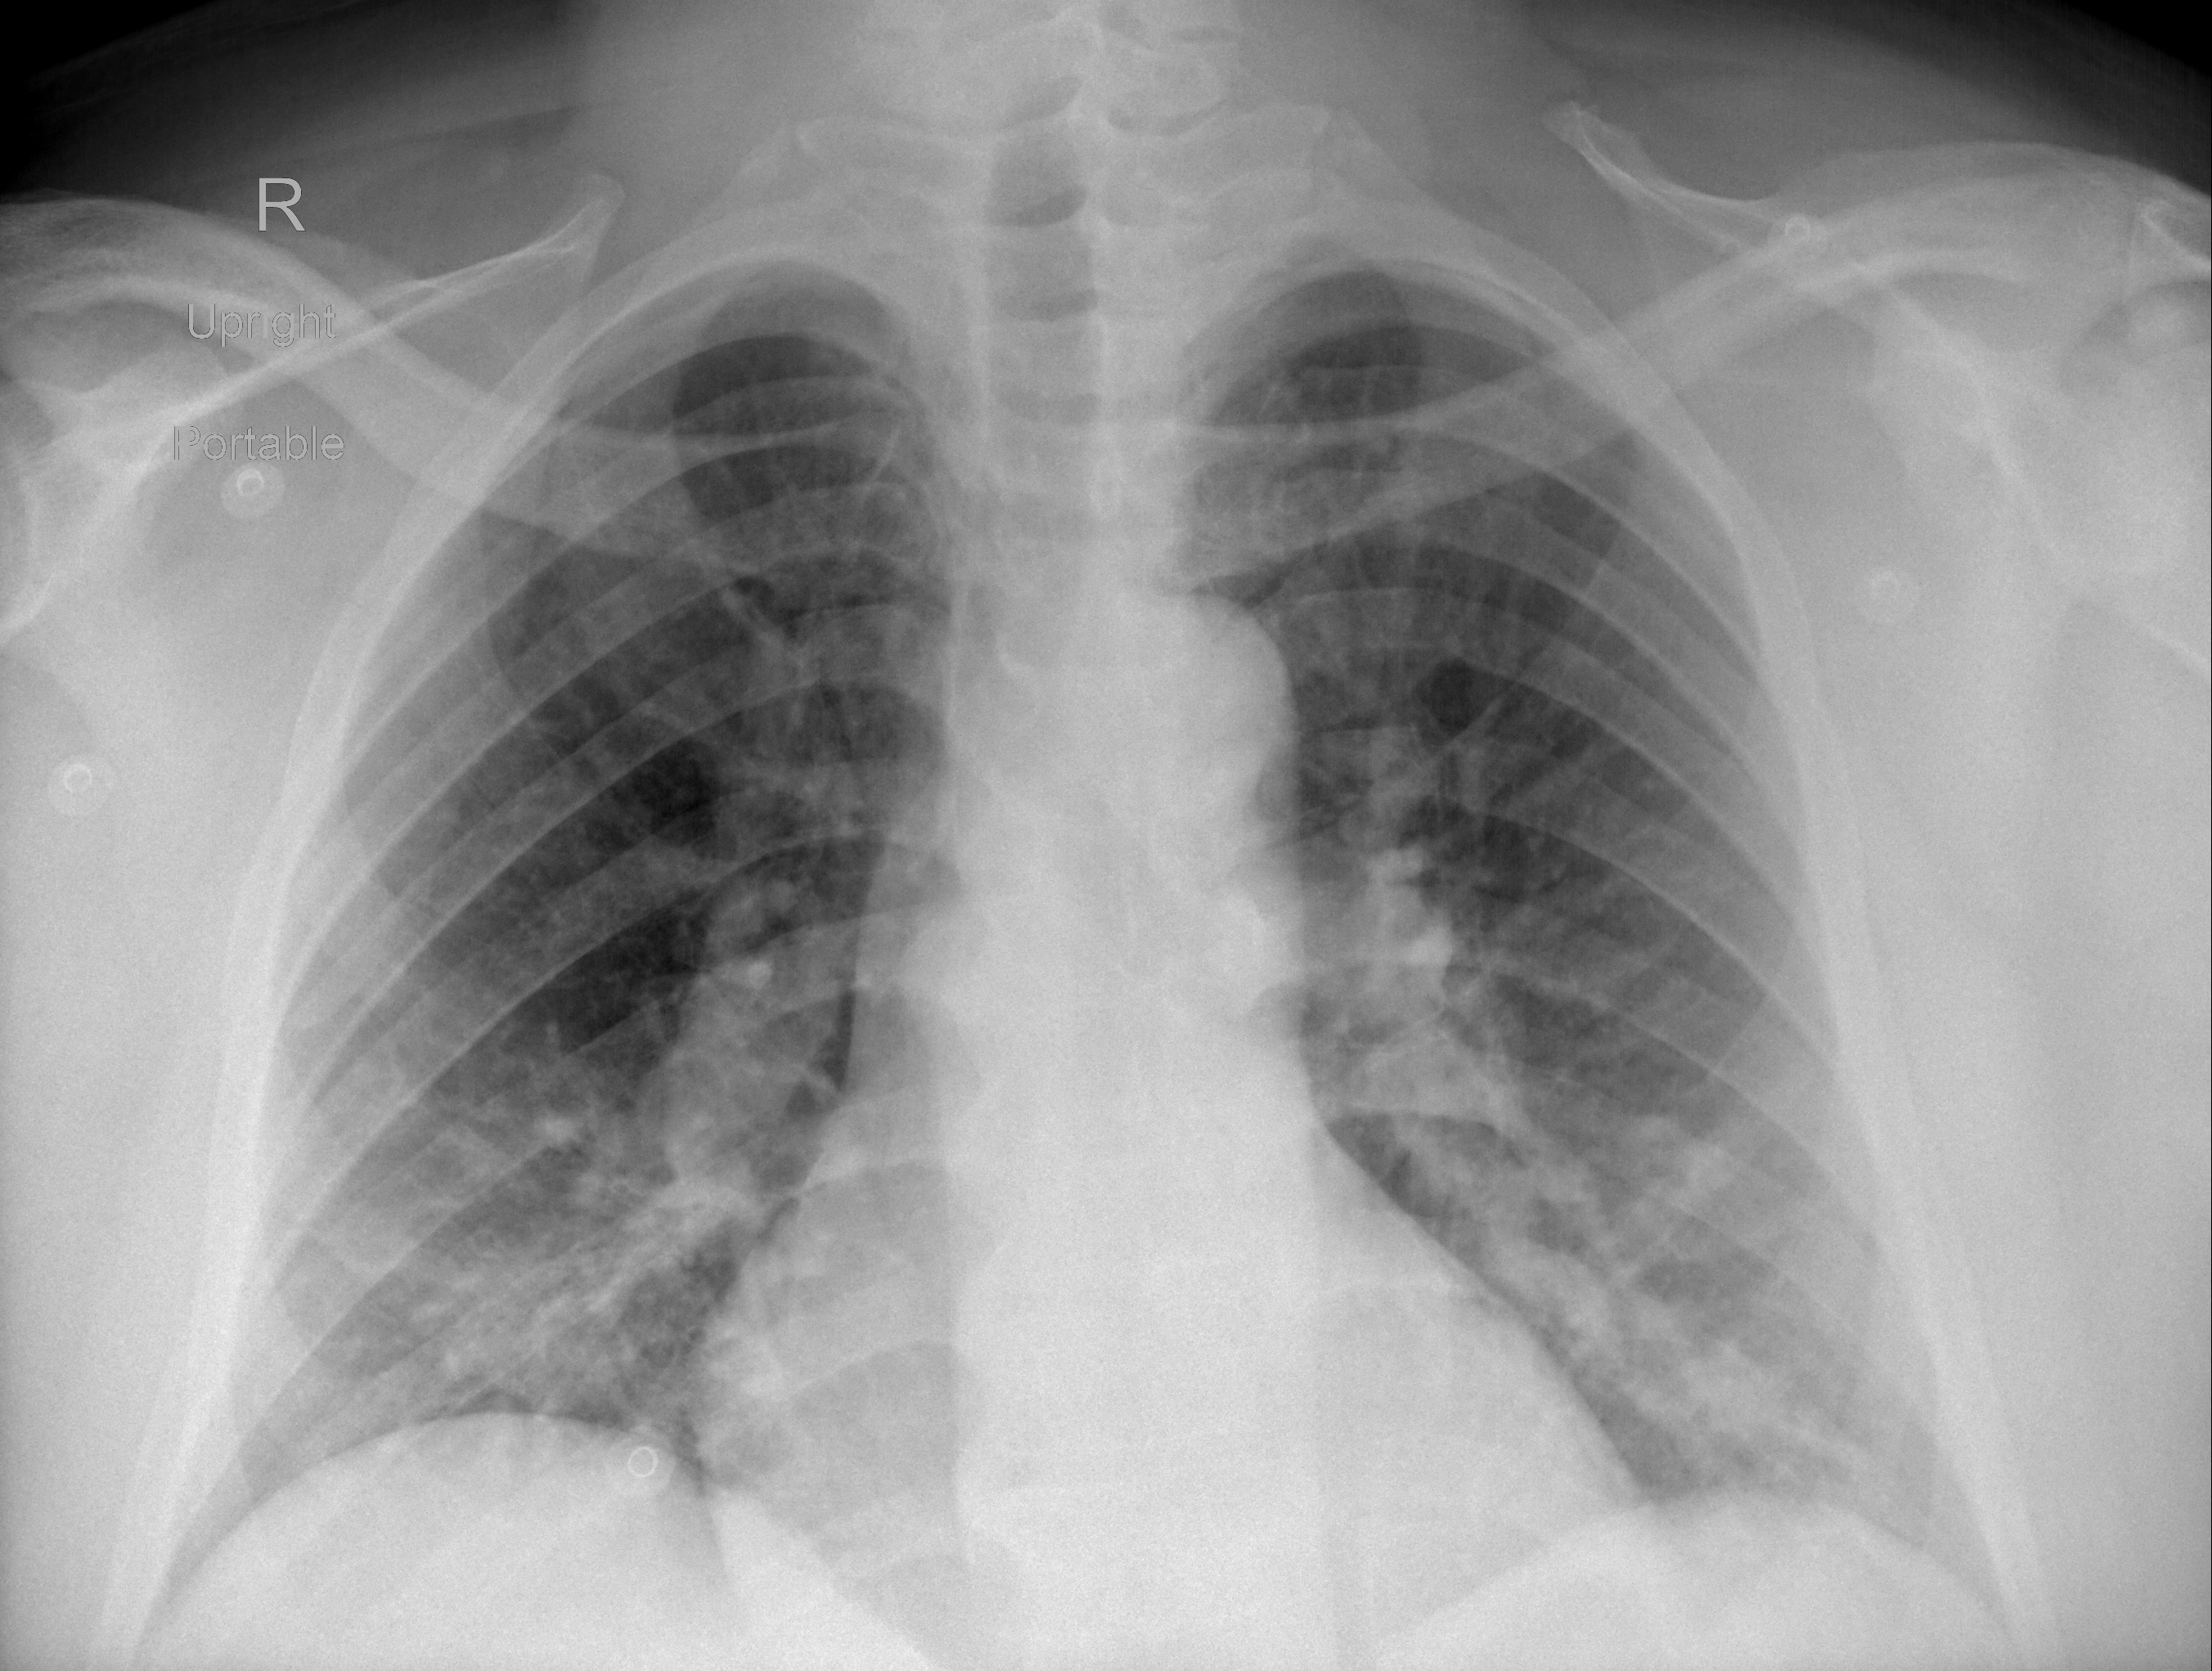
Chest X-ray (portable), AP projection. Male patient, age 47 years; imaged 1 day after the COVID-19 diagnosis.
Radiologist's key findings for this exam: Ill-defined bilateral lower lung airspace opacities are again demonstrated, mildly worsened on this exam.